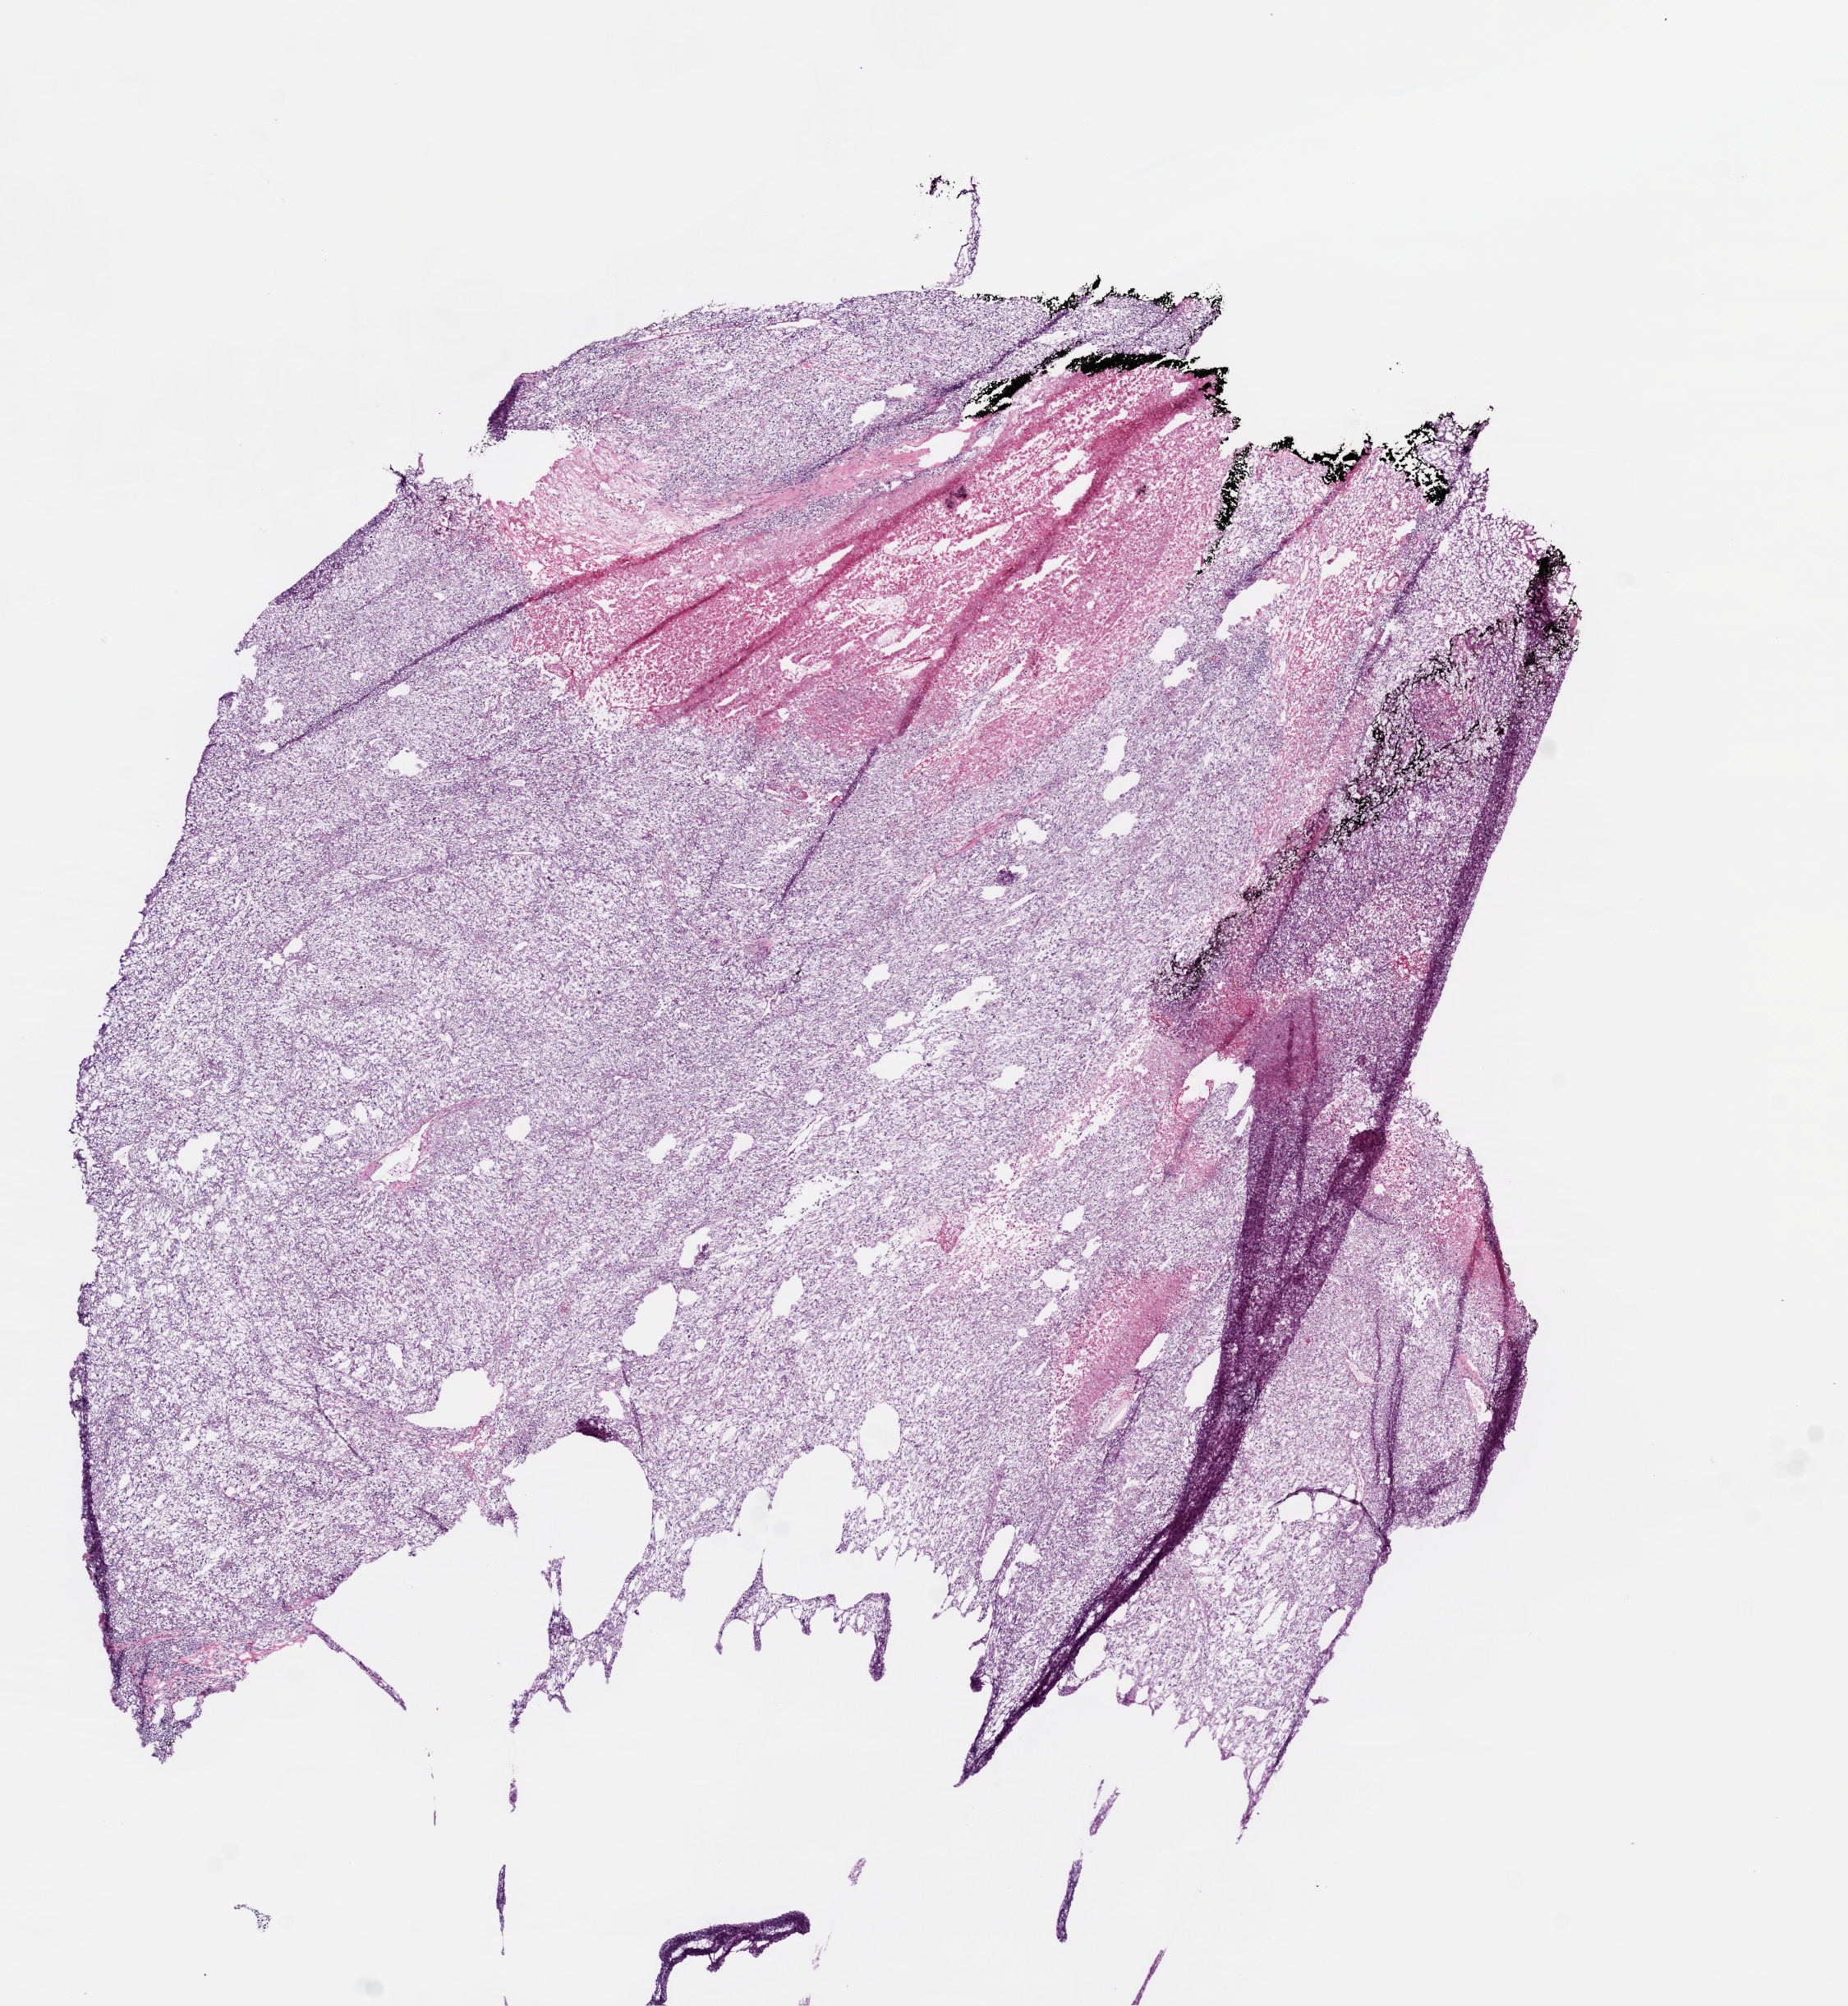
Hematoxylin and eosin (H&E) stained whole-slide image, a low-resolution overview of the entire scanned area, about 9.0 x 9.8 mm; frozen section; primary tumour sample from the kidney. Patient: male, age at initial diagnosis 70 years. Slide review estimates, as recorded: tumour cells 85%, tumour nuclei 85%.
Histologic diagnosis: Clear cell adenocarcinoma, NOS.